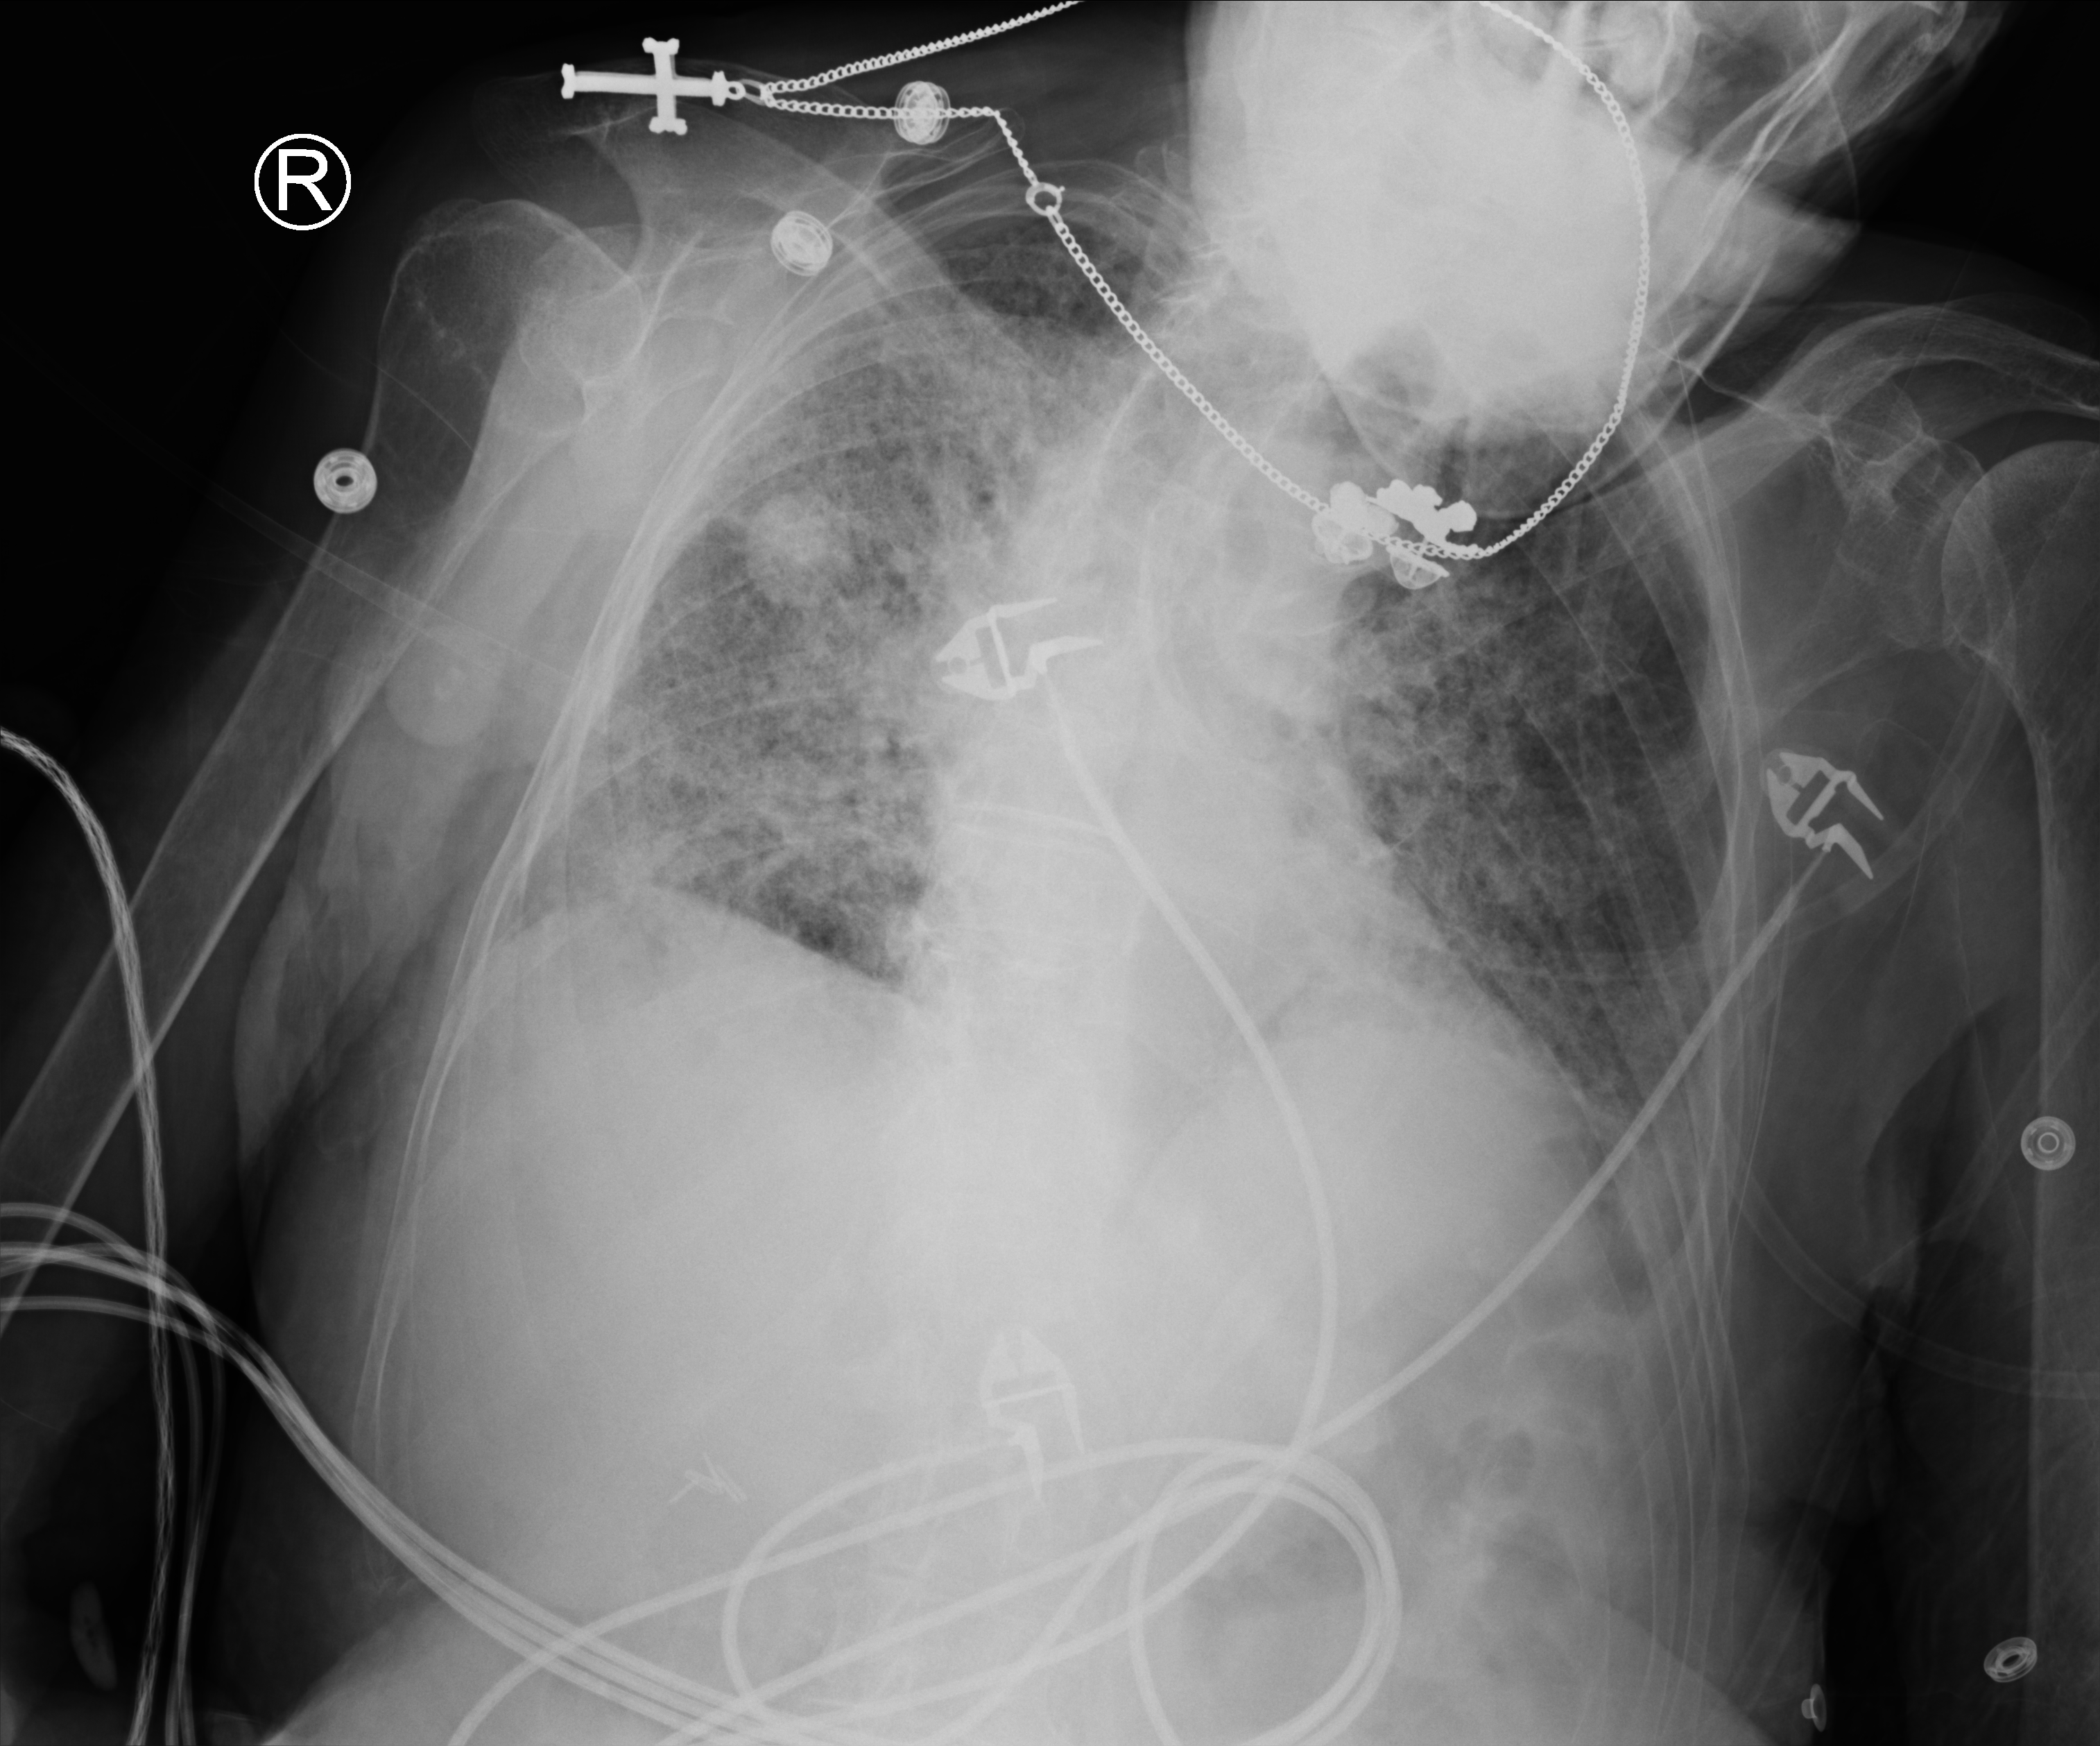
Portable chest radiograph, anteroposterior (AP) projection. Female patient hospitalised with COVID-19, age 75–90 years.
Admission-level facts for this patient (not findings on this image; timing relative to this image not recorded):
- mechanically ventilated during this hospital stay: no
- admitted to intensive care during this hospital stay: no